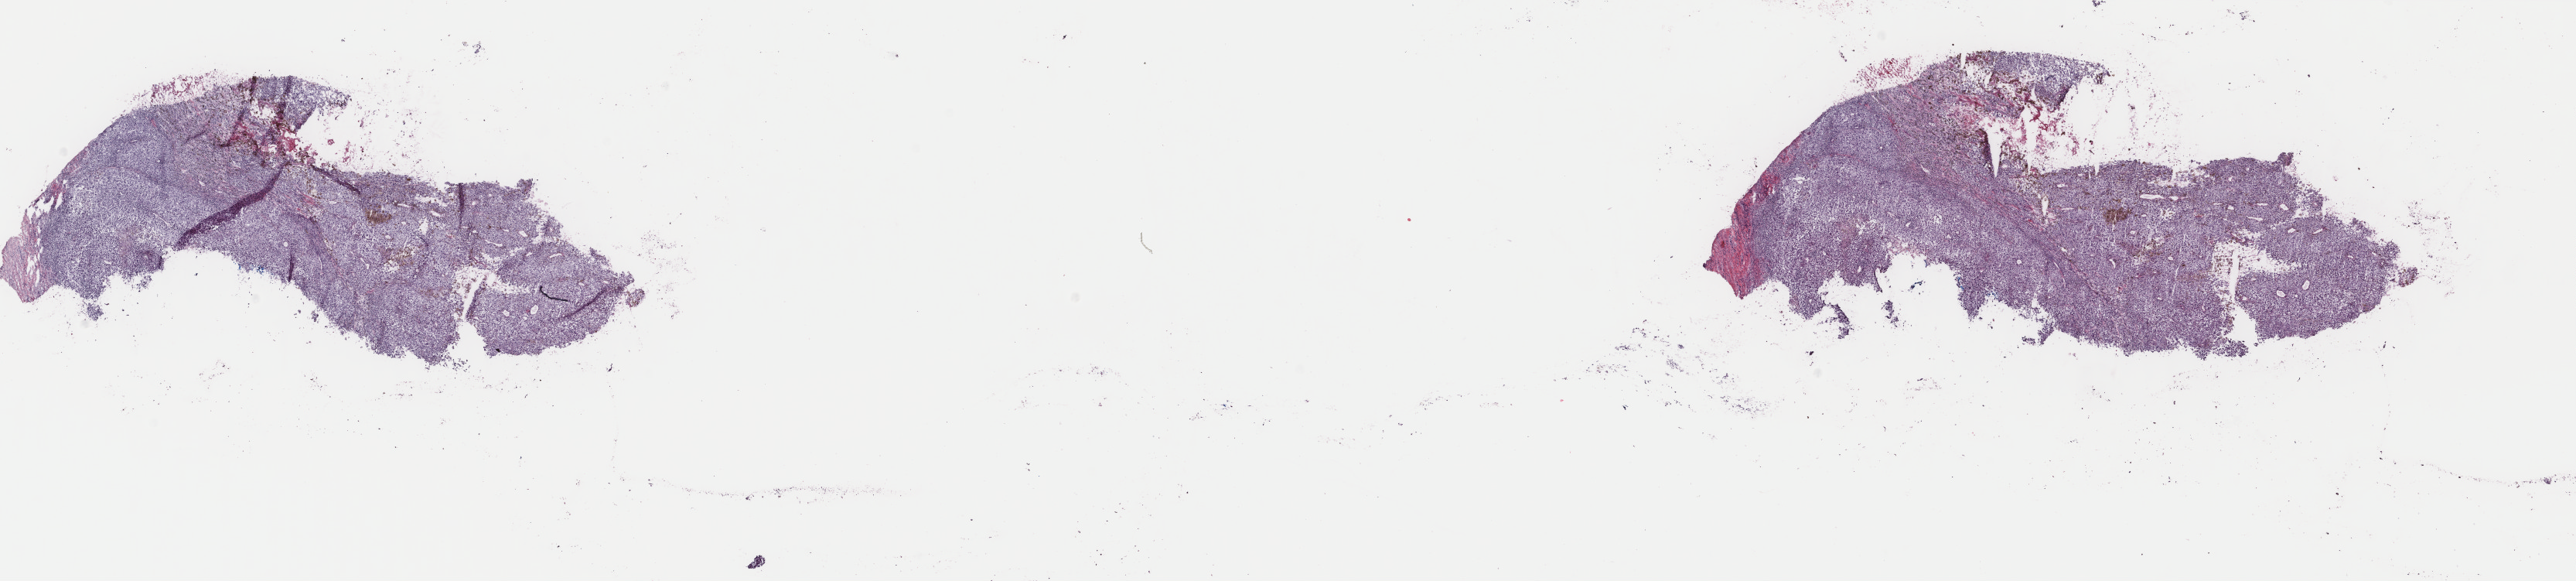
Whole-slide histology image, H&E-stained, whole scanned area (about 26.4 x 6.0 mm, slide scanned at 40x) shown as a low-resolution overview, frozen section, metastatic tumour sample, sampled site not recorded. Female patient; age at initial diagnosis 75 years. Slide review estimates, as recorded: tumour cells 97%, tumour nuclei 60%, normal cells 1%, stromal cells 0%, necrosis 2%. Inflammatory infiltration, as recorded: lymphocyte infiltration 40%, monocyte infiltration 0%, neutrophil infiltration 0%.
* this section: metastatic tumour tissue
* patient diagnosis: Malignant melanoma, NOS